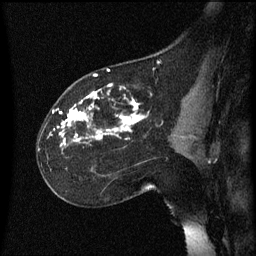
Breast MRI (dynamic contrast-enhanced), one sagittal slice. Position 36 of 60 along the scan axis. Dynamic contrast-enhanced series, image 2 of 3 at this slice position (ordered by acquisition). 1.5 T. TE 4.2 ms, TR 8.4 ms. 2.2 mm slice thickness. 256 × 256 image matrix. Patient: female, 35 years. From the clinical record (not read from this slice): setting: breast cancer imaged before/during neoadjuvant chemotherapy; receptor status: HER2-positive.
Annotated regions visible in this slice (semi-automatic segmentation, software-assisted and operator-edited):
- analysis volume of interest (the breast-tissue region the enhancement analysis was run in; not a lesion): bounding box <37,72,178,173> (left, top, right, bottom; pixels)
- tumour enhancement mask (voxels above the 70 % enhancement threshold inside the analysis volume of interest): <54,84,146,145>